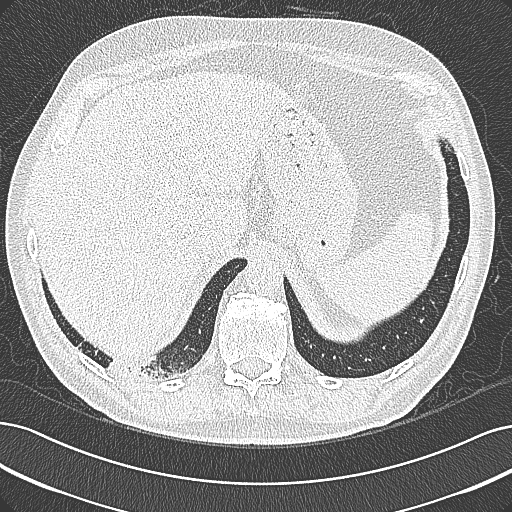
Low-dose screening chest CT, axial slice; baseline screening round; lung window (W 1500 / L -600 HU); lung (sharp) reconstruction kernel (B80f); slice 263 of 355 in the series. Male participant, aged 68 years at enrolment. Former smoker at enrolment.
Lesion marked by an expert reader, bounding box [x1, y1, x2, y2] px = [93, 336, 197, 396]. No non-calcified nodule or mass ≥4 mm was recorded by the screening reader at this exam. Later outcome: lung cancer diagnosed 154 days after this screen — mucinous adenocarcinoma, right lower lobe, well differentiated (G1), stage IB (AJCC 6th edition), 50 mm at pathology.